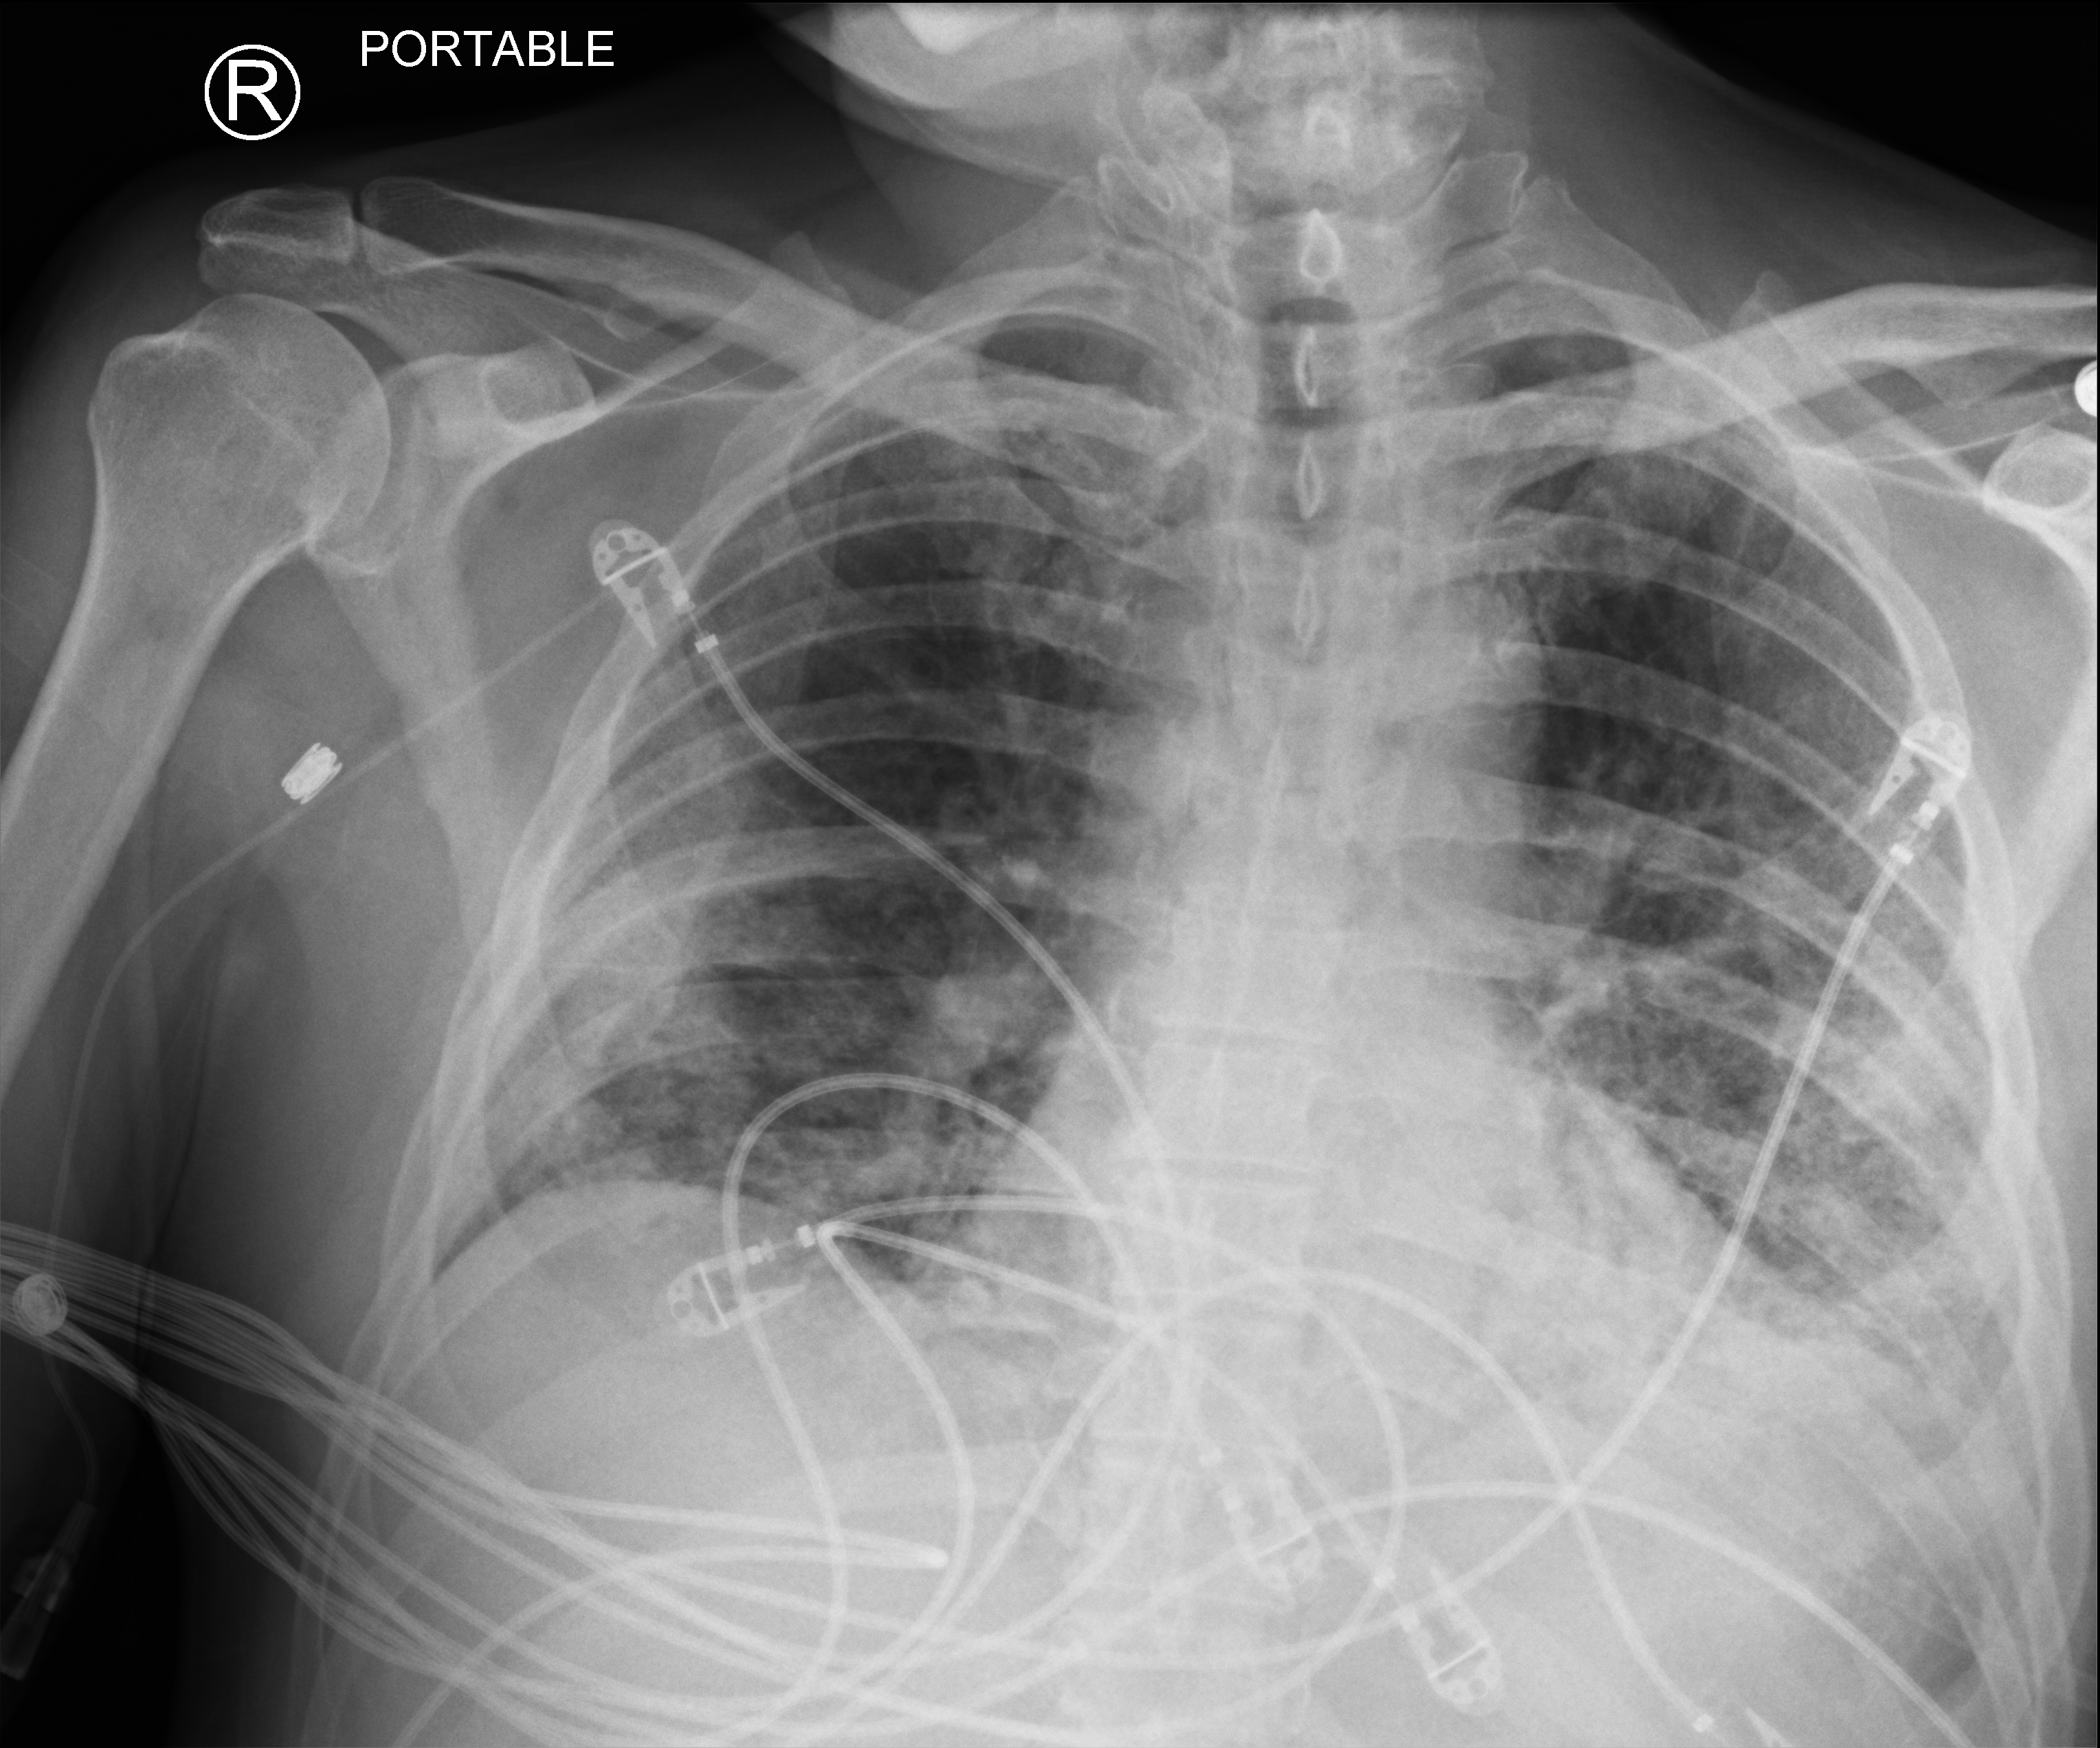
Portable chest radiograph. Male patient hospitalised with COVID-19, age 60–74 years.
Hospital-stay facts (about this admission, not read from this image; timing relative to this image not recorded): mechanically ventilated during this hospital stay: yes; admitted to intensive care during this hospital stay: yes.